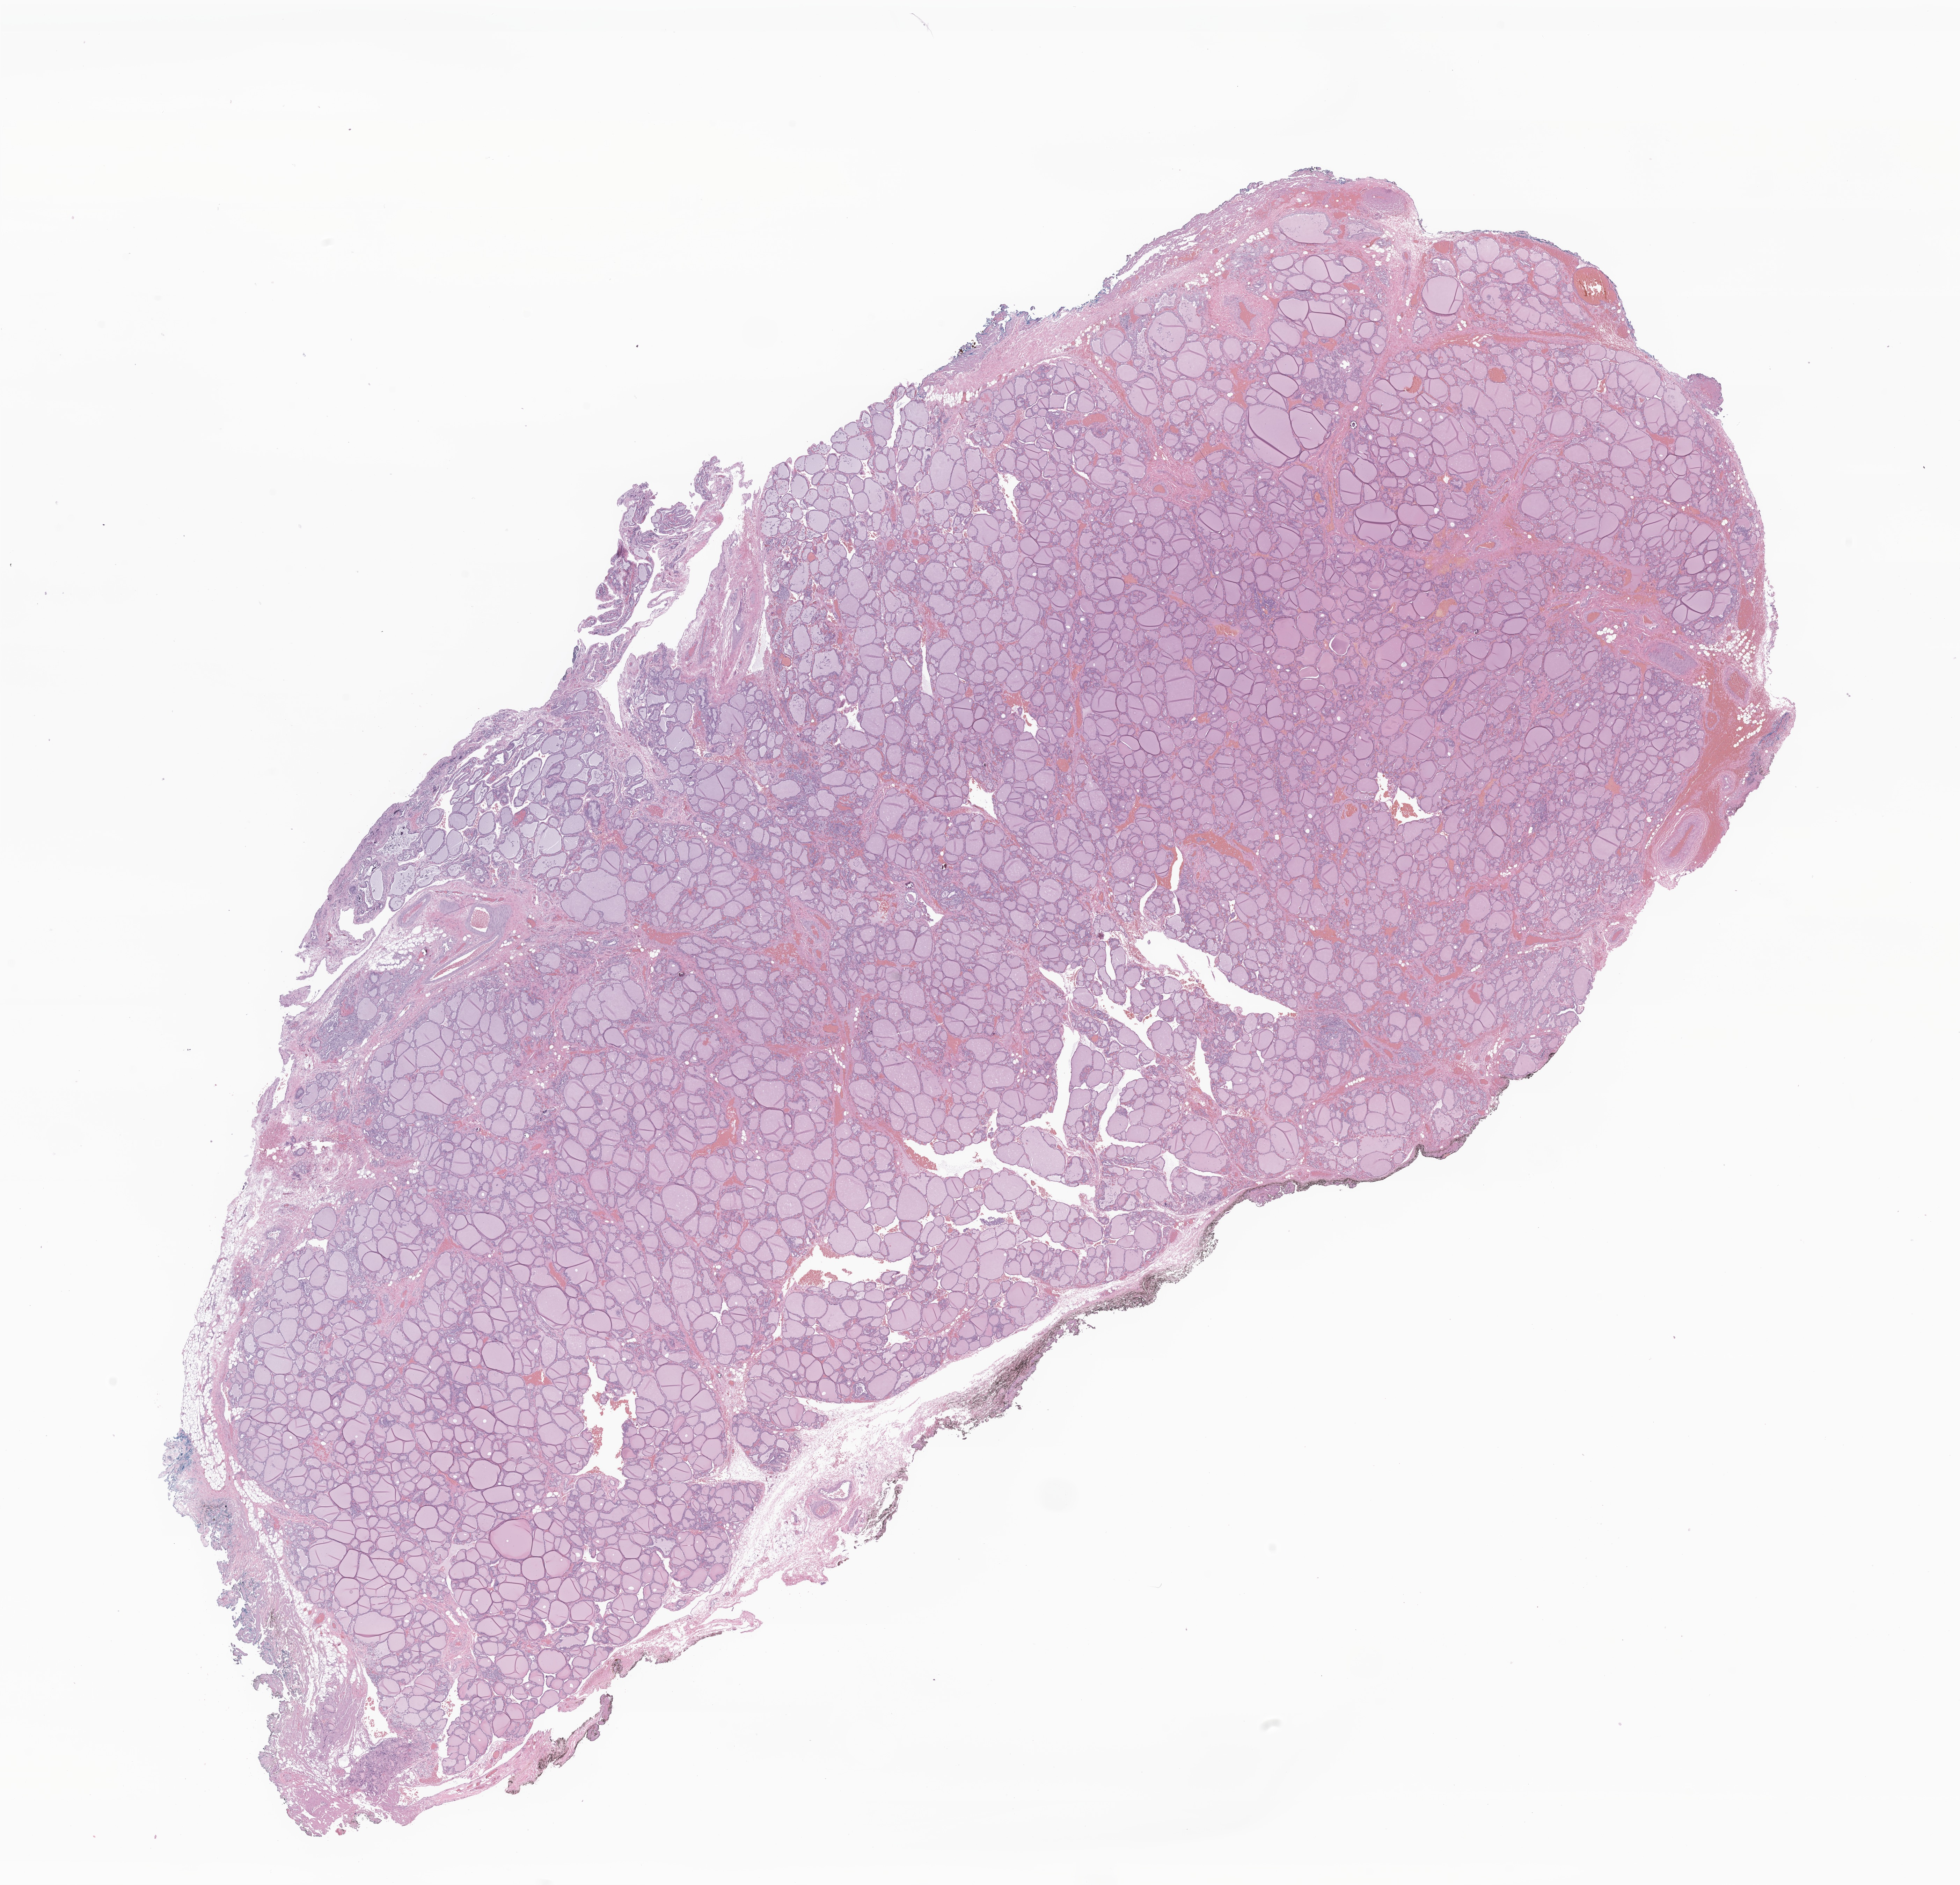
Digitized haematoxylin and eosin-stained section of tumor tissue from the thyroid — low-resolution overview of the scanned area, about 23.7 x 22.7 mm, formalin-fixed paraffin-embedded section. Patient: female, age 216 months (18 years).
Recorded diagnosis: Papillary carcinoma, NOS.